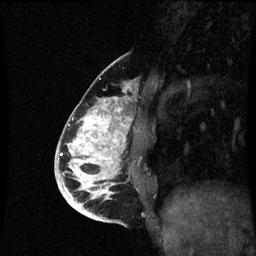
Breast MRI (dynamic contrast-enhanced), one sagittal slice. Position 24 of 60 along the scan axis. Dynamic contrast-enhanced series, image 2 of 3 at this slice position (ordered by acquisition). 1.5 T. TE 4.2 ms, TR 8.9 ms. 256 × 256 image matrix. Patient: female, 35 years. From the clinical record (not read from this slice): setting: breast cancer imaged before/during neoadjuvant chemotherapy; receptor status: HR-positive, HER2-negative.
Annotated regions visible in this slice (semi-automatic segmentation, software-assisted and operator-edited):
- analysis volume of interest (the breast-tissue region the enhancement analysis was run in; not a lesion): bounding box [x1, y1, x2, y2] px = [66, 98, 136, 215]
- tumour enhancement mask (voxels above the 70 % enhancement threshold inside the analysis volume of interest): [66, 98, 128, 215]